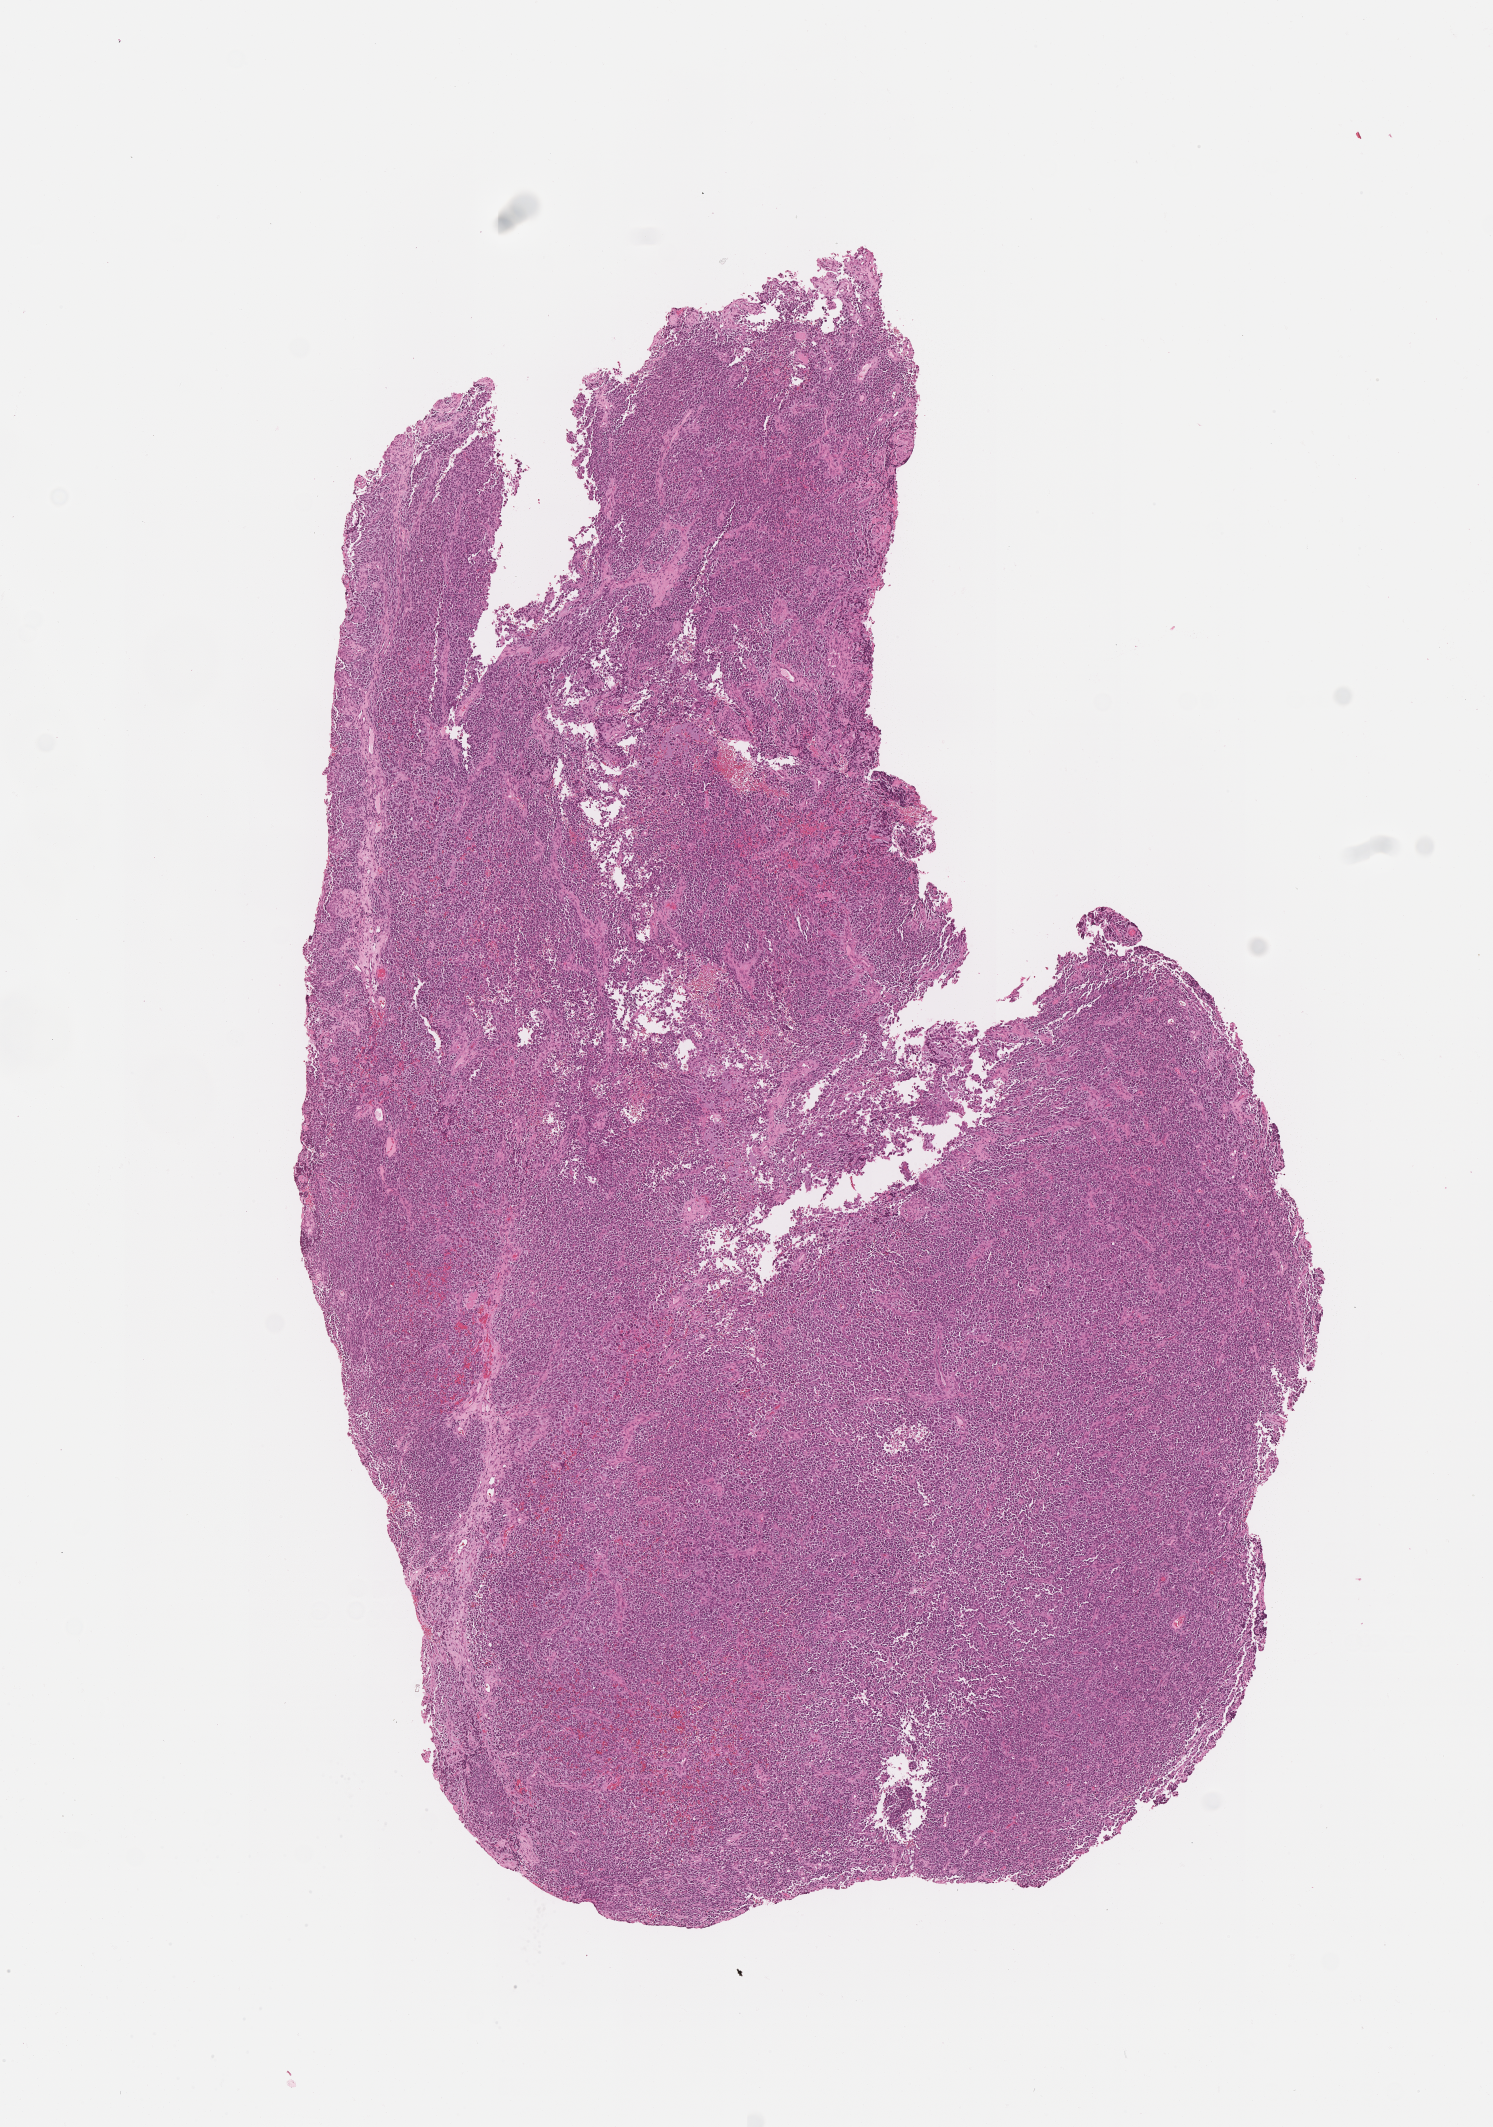
Digitized haematoxylin and eosin-stained section of tumor tissue, low-resolution overview of the scanned area, about 6.0 x 8.6 mm; formalin-fixed paraffin-embedded section; site: lung-right. Patient: male, age 3.8 years at diagnosis.
- stage (as recorded): 3
- diagnosis: rhabdomyosarcoma; histological classification: alveolar rhabdomyosarcoma
- primary site (case record): lung & other sites